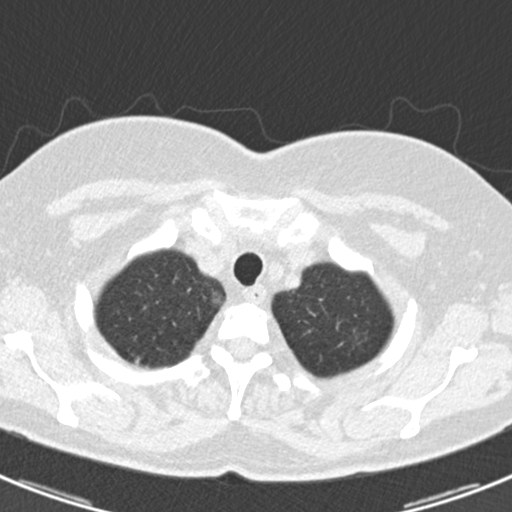
Low-dose screening chest CT, axial slice; baseline annual screen; lung window (W 1500 / L -600 HU); standard (soft-tissue) reconstruction kernel (B30f); 512 × 512 image matrix. Female participant, aged 60 years at enrolment. Current smoker at enrolment.
Lesion marked by an expert reader, box from (x=334, y=319) to (x=380, y=362) px. The screening reader recorded 3 non-calcified nodules or masses ≥4 mm on this exam (lingula, left lower lobe, lingula); which of them this box marks is not recorded. Official screen result: positive, change unspecified: nodule(s) >= 4 mm or enlarging nodule(s), mass(es), or other non-specific abnormalities suspicious for lung cancer. Later outcome: lung cancer diagnosed 886 days after this screen (after the third annual screen) — non-small cell carcinoma, left upper lobe, poorly differentiated (G3), stage IB (AJCC 6th edition), 7 mm at pathology.